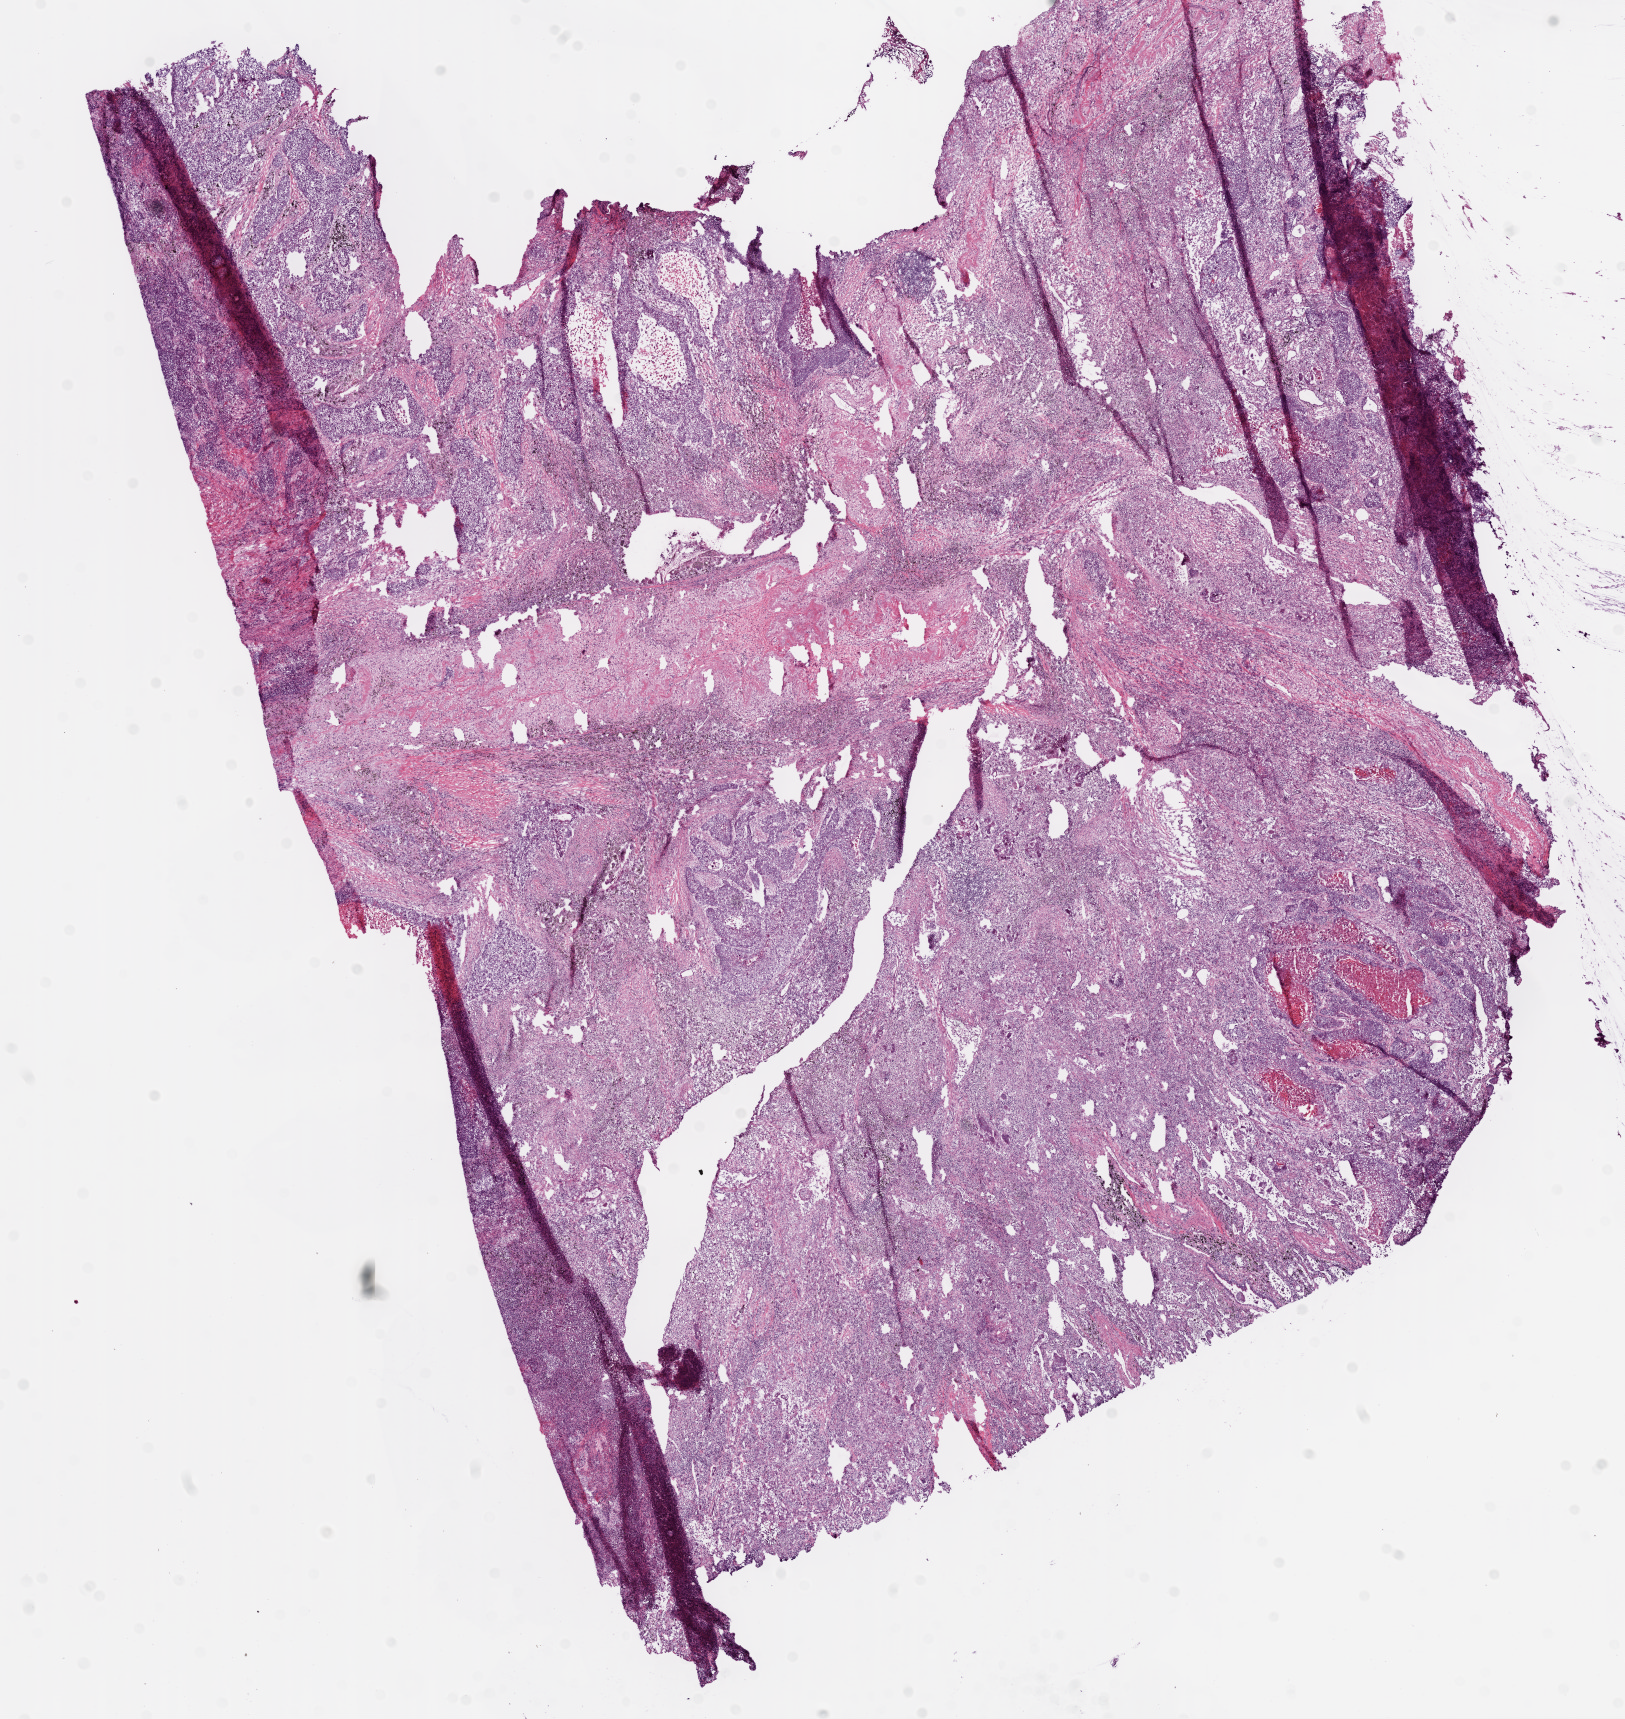
H&E whole-slide image, whole scanned area (about 13.0 x 13.8 mm, acquisition: 20x scan) shown as a low-resolution overview; frozen section; sample: primary tumour, lung. Male, age 69 years at initial diagnosis. Pathologist review of this section (percent, as recorded): tumour cells 70%, tumour nuclei 60%, normal cells 0%, stromal cells 20%, necrosis 10%.
Laterality: left. AJCC pathologic stage: IB (6th edition). Diagnosis: Squamous cell carcinoma, NOS (upper lobe, lung).